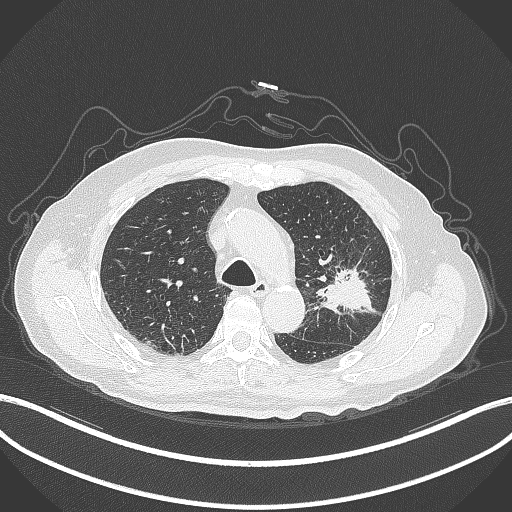
Chest CT, one axial slice. Slice 207 of 331 in the series (ordered by position). Reconstruction kernel B70f. Lung window (W 1500 / L -600 HU). 1 mm slice thickness. 512 × 512 image matrix, field of view 400 × 400 mm. Patient: male, 79 years. Case-level facts recorded for this patient, not image findings: clinical TNM (as recorded): T2a N1 M1; histopathological grade: G3.
Annotated regions visible in this slice (rectangle marked by the reading radiologist):
- lung tumour (recorded histology: adenocarcinoma): bounding box [x1, y1, x2, y2] px = [314, 261, 384, 318]